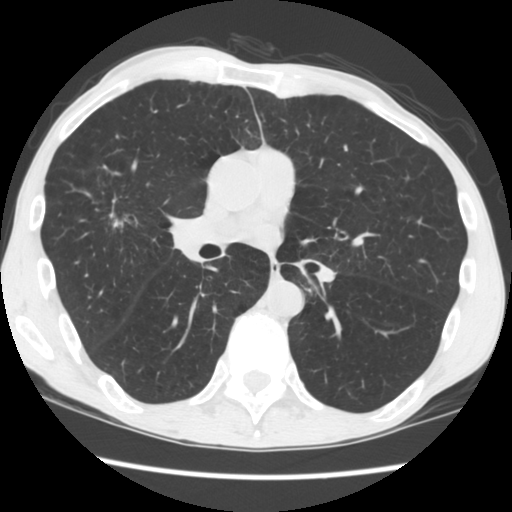
Axial slice from a low-dose chest CT screening exam. Second annual screen. Lung window (W 1500 / L -600 HU). 2.5 mm slice thickness. Standard (soft-tissue) reconstruction kernel (STANDARD). 120 kVp. Slice 89 of 181 in the series. Male participant, aged 56 years at enrolment.
Expert reader's lesion annotation, bounding box <78,152,147,234> (left, top, right, bottom; pixels). The screening reader recorded 2 non-calcified nodules or masses ≥4 mm on this exam (right upper lobe, left upper lobe); which of them this box marks is not recorded. Official screen result: positive, change unspecified: nodule(s) >= 4 mm or enlarging nodule(s), mass(es), or other non-specific abnormalities suspicious for lung cancer. Participant outcome: lung cancer diagnosed 101 days after this screen — squamous cell carcinoma, NOS, right upper lobe, right middle lobe, well differentiated (G1), stage IA (AJCC 6th edition), 27 mm at pathology.